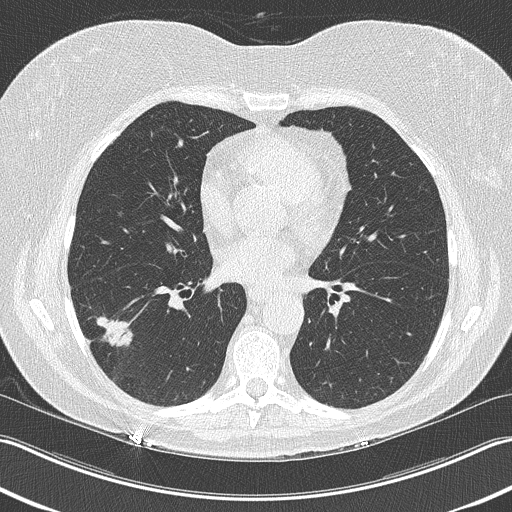
Low-dose screening chest CT, one axial slice. Reconstruction kernel B50f. Lung window (W 1500 / L -600 HU). 2 mm slice thickness. 512 × 512 image matrix, field of view 348 × 348 mm.
Structures marked on this image (expert manual segmentation):
- lesion 1 (tumor, lower lobe of right lung): bounding box [x1, y1, x2, y2] px = [96, 316, 133, 347]